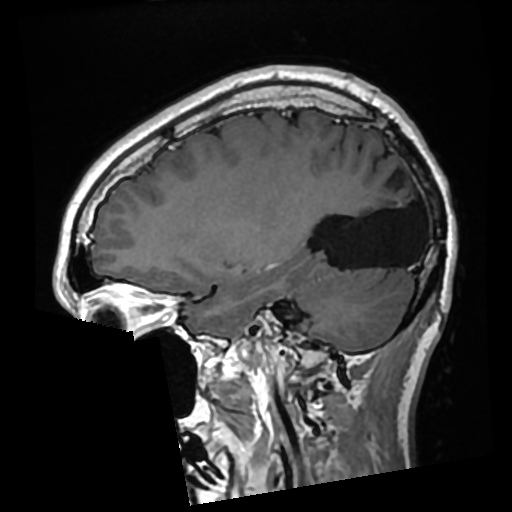
Brain MRI from a brain-tumour surgery series, one sagittal slice; position 101 of 276 along the scan axis; T1-weighted post-contrast; 512 × 512 image matrix, field of view 250 × 250 mm. Case-level facts recorded for this patient, not image findings: histopathology: Glioma with ependymal features; WHO grade: 2.
Annotated regions visible in this slice (expert manual segmentation):
- previous resection cavity: bounding box <327,182,423,268> (left, top, right, bottom; pixels)
- tumour: <399,202,402,206>